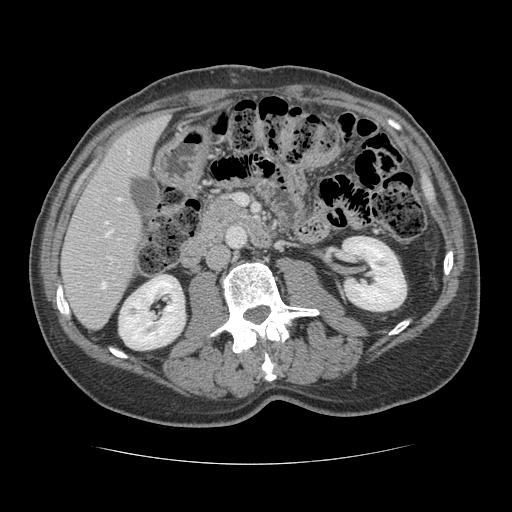
Contrast-enhanced abdominal CT, one axial slice; position 51 of 134 along the scan axis; reconstruction kernel STANDARD; 120 kVp; intravenous contrast given; soft-tissue window (W 400 / L 40 HU); 512 × 512 image matrix, field of view 377 × 377 mm. Male patient, age 68 years. Case-level facts recorded for this patient, not image findings: diagnosis: colorectal cancer liver metastases, imaged before liver resection; multiple liver metastases: yes; largest metastasis: 2.2 cm; disease in both lobes: no.
Outlined on this slice (outlined manually by an expert reader):
- hepatic veins: box from (x=105, y=150) to (x=129, y=236) px
- liver: (x=63, y=116)–(x=167, y=329)
- planned liver remnant (the part of the liver to remain after resection): (x=63, y=116)–(x=167, y=329)
- portal vein (with intrahepatic branches): (x=101, y=257)–(x=112, y=288)